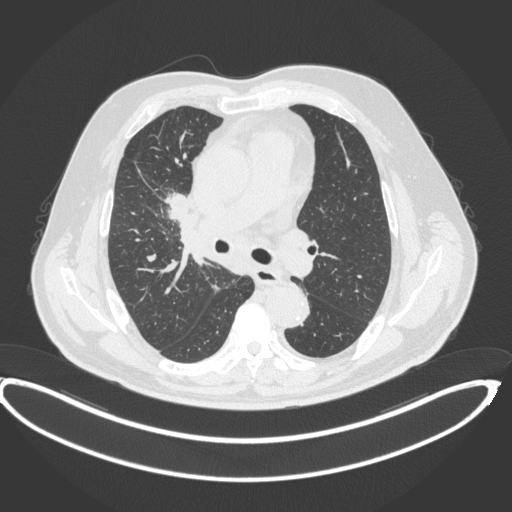
Chest CT, one axial slice. Slice 249 of 395 in the series (ordered by position). Reconstruction kernel B31f. 120 kVp. Lung window (W 1500 / L -600 HU). 1 mm slice thickness. 512 × 512 image matrix. Patient: male, 62 years. From the clinical record (not read from this slice): clinical TNM (as recorded): T1c N3 M1c.
Structures marked on this image (rectangle marked by the reading radiologist):
- lung tumour (recorded histology: adenocarcinoma): bounding box <166,189,199,227> (left, top, right, bottom; pixels)